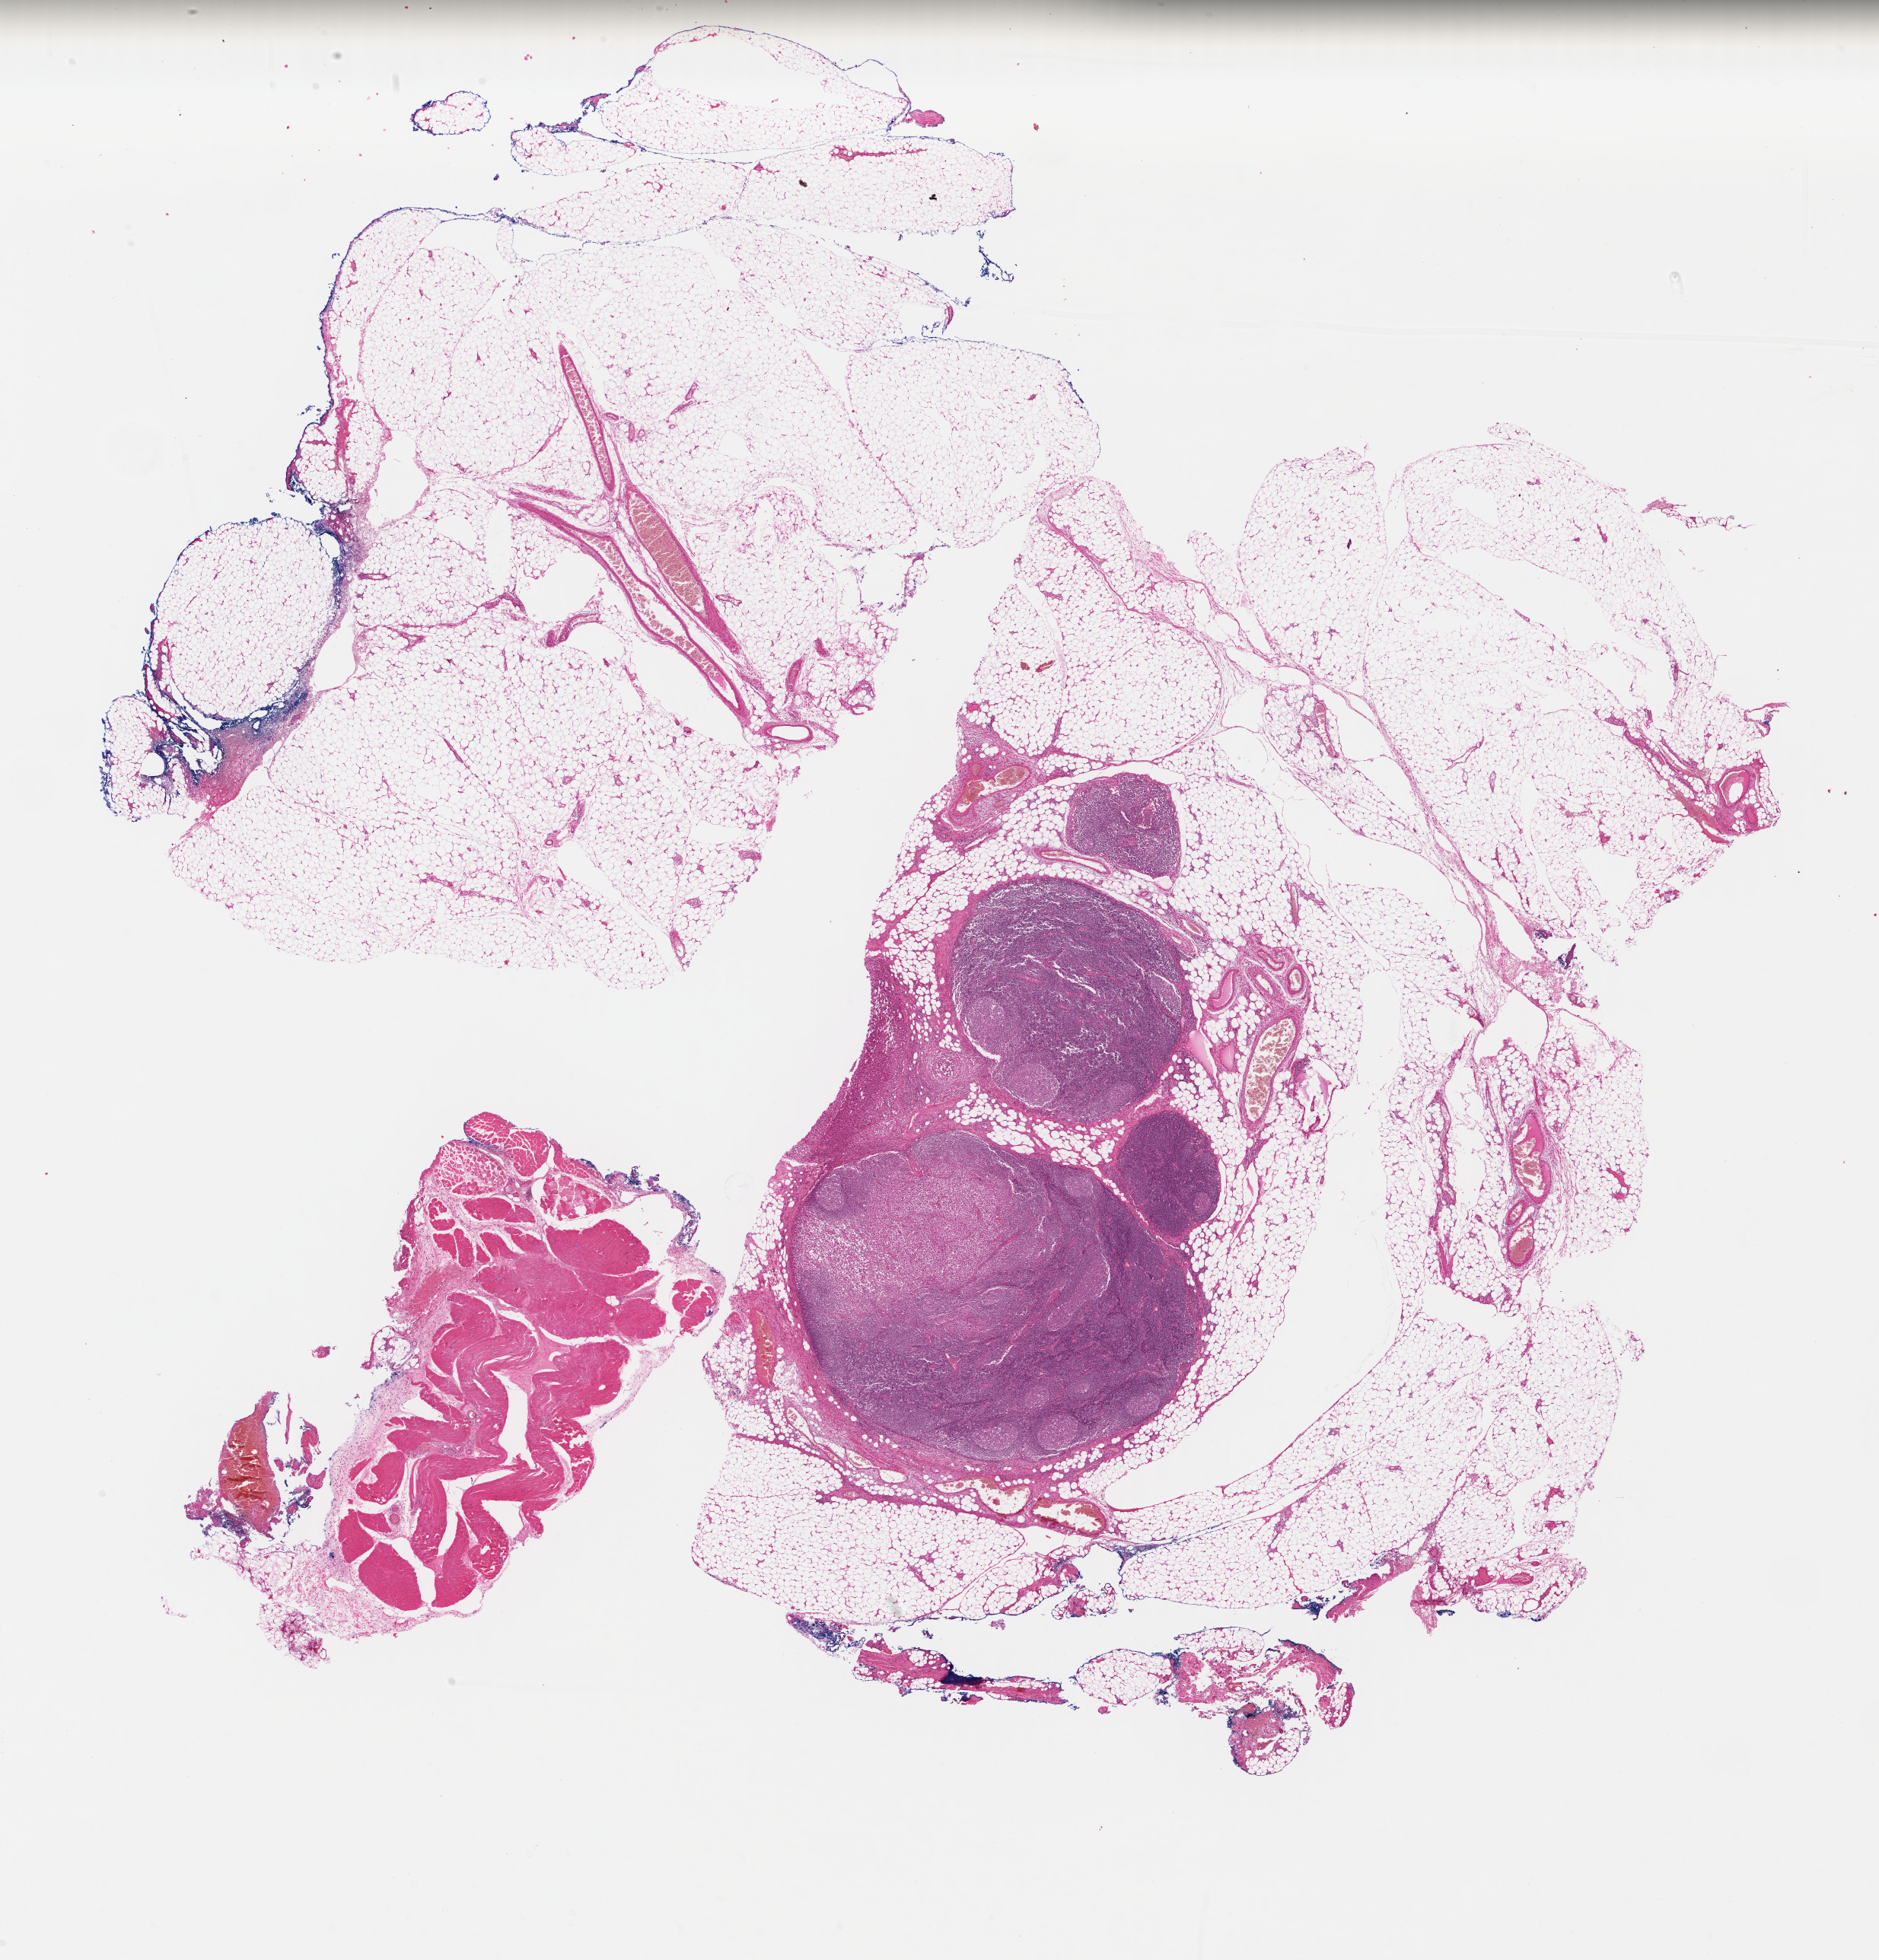
H&E whole-slide image, shown as a low-resolution overview of the whole scanned area (about 19.4 x 20.2 mm, acquisition: 40x scan), FFPE section, sample: primary tumour, skin. Male, age 49 years at initial diagnosis.
• histologic diagnosis: Malignant melanoma, NOS